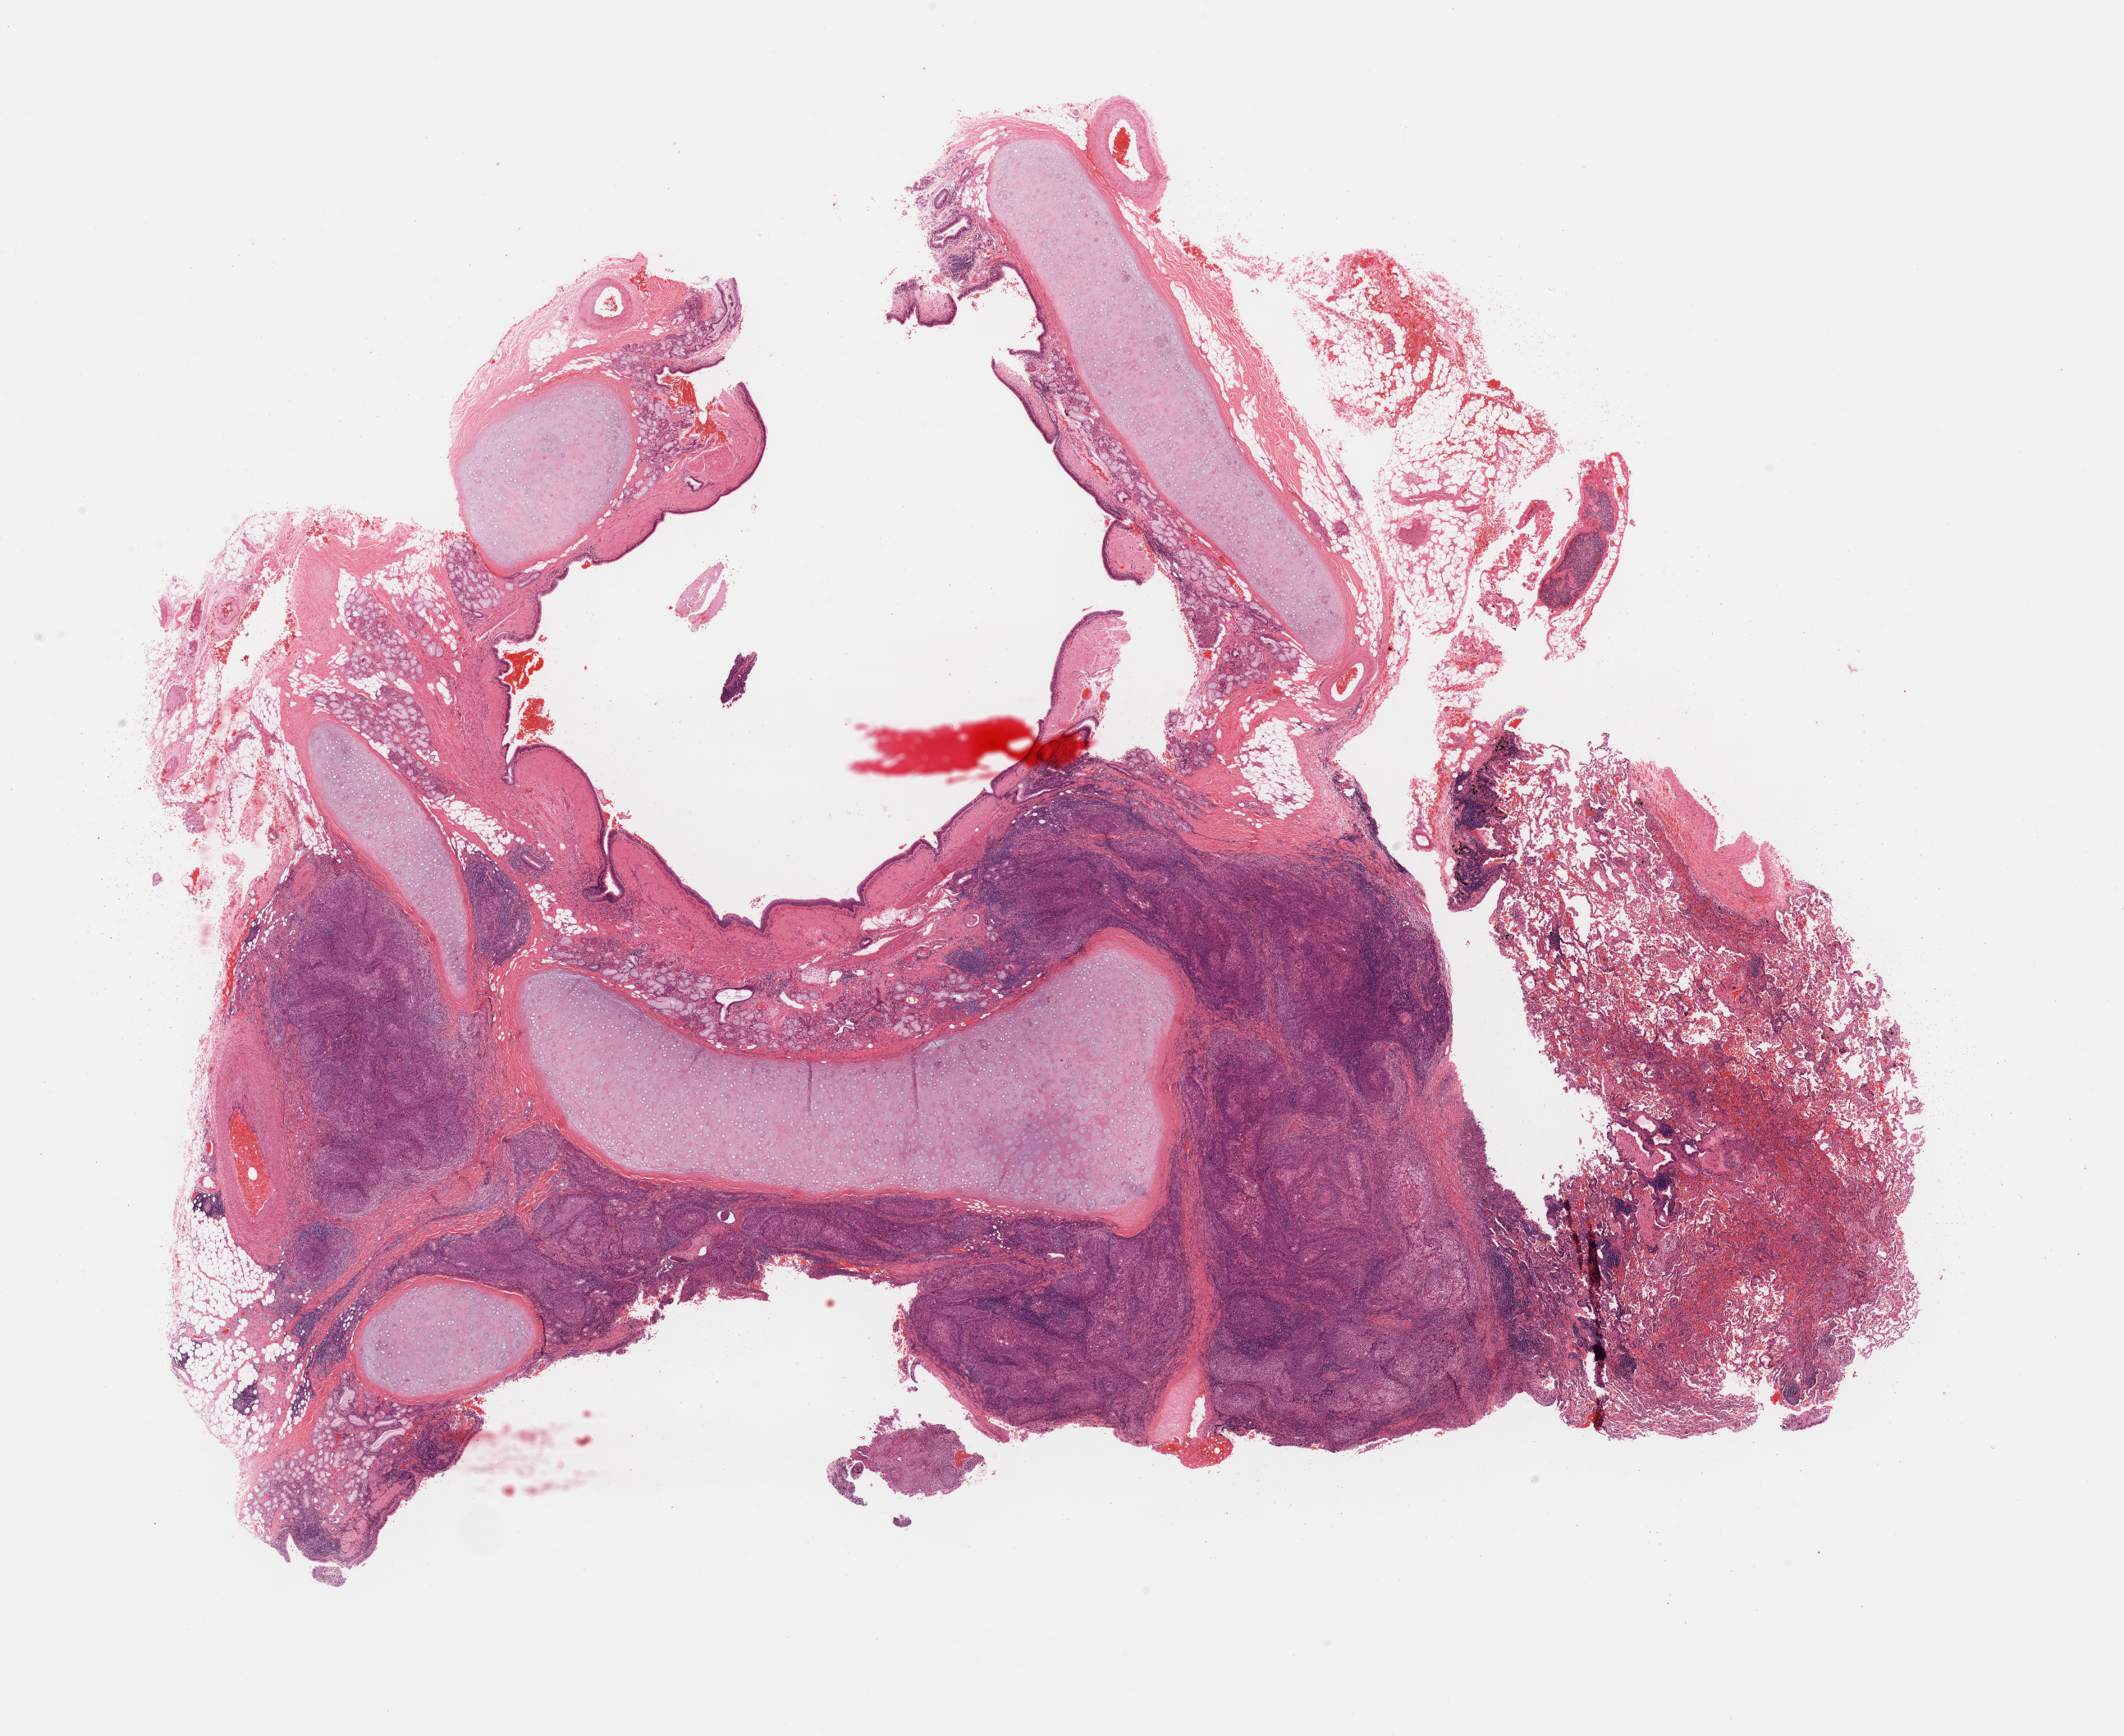
H&E whole-slide image, a low-resolution overview of the entire scanned area, about 20.4 x 16.7 mm (from a 40x scan). Formalin-fixed paraffin-embedded (FFPE) diagnostic section. Sample: primary tumour, lung. Male, age 65 years at initial diagnosis.
Pathologic diagnosis: Squamous cell carcinoma, NOS.